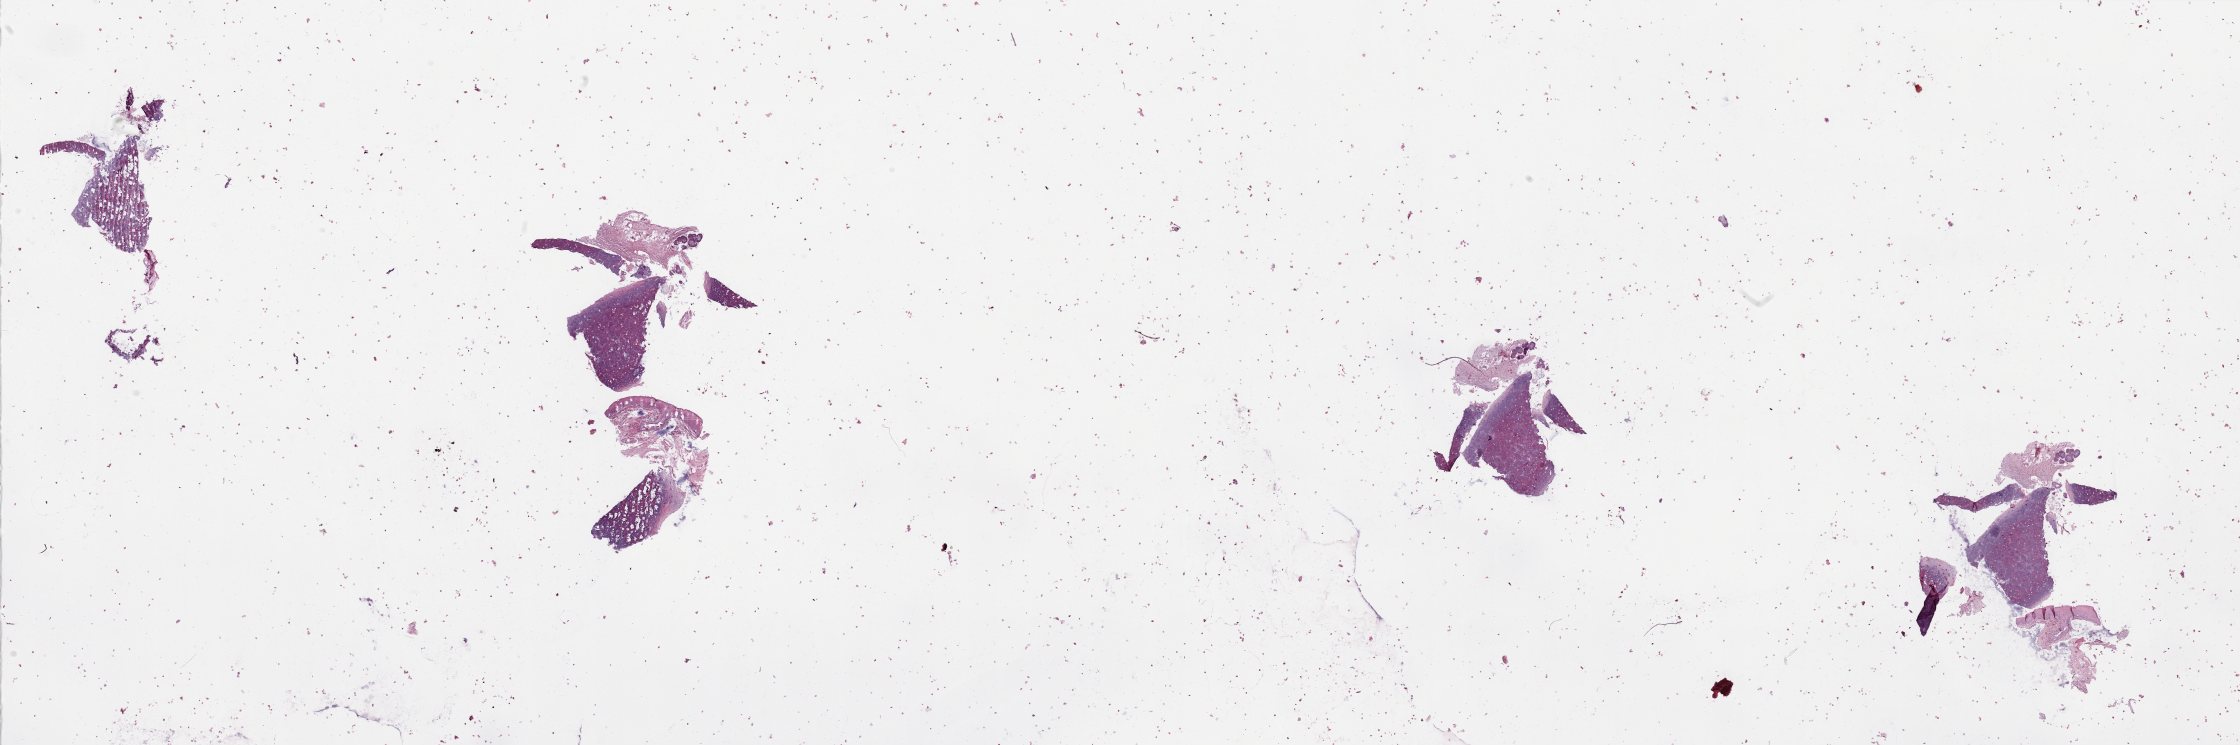
Whole-slide histology image, H&E, shown as a low-resolution overview of the whole scanned area (about 35.4 x 11.8 mm, slide scanned at 20x). Normal (non-tumour) tissue sample, sampled site: larynx. 50-year-old male patient.
- this section: normal (non-tumour) tissue from the same patient
- patient diagnosis: Squamous cell carcinoma, NOS (larynx, NOS)